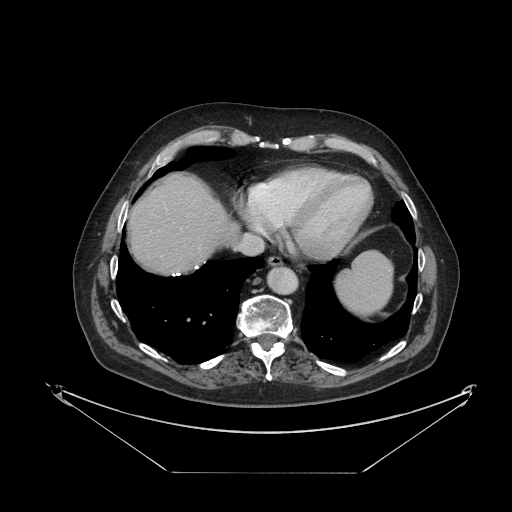
Contrast-enhanced abdominal CT, one axial slice; position 109 of 121 along the scan axis; 120 kVp; intravenous contrast given; soft-tissue window (W 400 / L 40 HU); 512 × 512 image matrix, field of view 500 × 500 mm. Male patient, age 68 years. Case-level facts recorded for this patient, not image findings: diagnosis: colorectal cancer liver metastases, imaged before liver resection; multiple liver metastases: no; largest metastasis: 4 cm; chemotherapy before resection: yes.
Annotated regions visible in this slice (expert manual segmentation):
- liver: bounding box [x1, y1, x2, y2] px = [131, 176, 234, 274]
- planned liver remnant (the part of the liver to remain after resection): [131, 176, 234, 274]